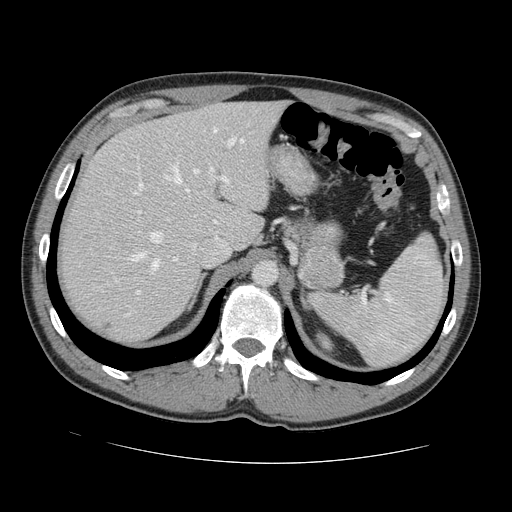
Contrast-enhanced abdominal CT, one axial slice; position 96 of 131 along the scan axis; 120 kVp; intravenous contrast given; soft-tissue window (W 400 / L 40 HU); 2.5 mm slice thickness; 512 × 512 image matrix, field of view 380 × 380 mm. Male patient, age 40 years. From the clinical record (not read from this slice): diagnosis: colorectal cancer liver metastases, imaged before liver resection; multiple liver metastases: yes; largest metastasis: 2.9 cm; disease in both lobes: yes.
Annotated regions visible in this slice (expert manual segmentation):
- hepatic veins: bounding box (x1, y1, x2, y2) in pixels: (126, 139, 244, 316)
- liver: (62, 102, 283, 343)
- planned liver remnant (the part of the liver to remain after resection): (99, 102, 284, 247)
- portal vein (with intrahepatic branches): (133, 137, 236, 295)
- liver metastasis: (105, 324, 112, 330)